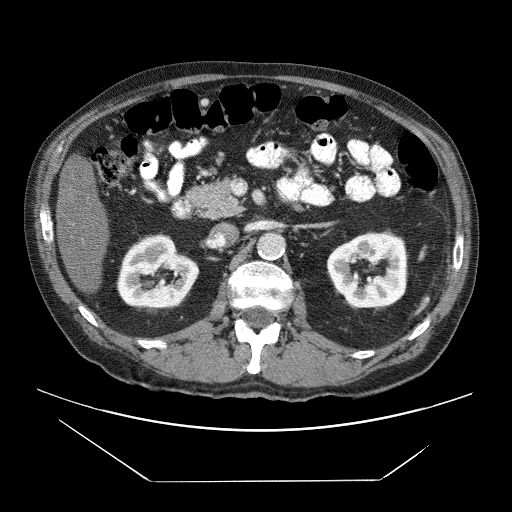
Contrast-enhanced abdominal CT (liver protocol), one axial slice; slice 17 of 83 in the series (ordered by position); 120 kVp; soft-tissue window (W 400 / L 40 HU); 2.5 mm slice thickness; 512 × 512 image matrix, field of view 420 × 420 mm. From the clinical record (not read from this slice): diagnosis: hepatocellular carcinoma (patient treated with transarterial chemoembolisation; whether this scan precedes or follows treatment is not stated here); TNM stage (as recorded): Stage-IVB; Child-Pugh class: B; tumour differentiation: poorly differentiated; tumour nodularity: uninodular.
Structures marked on this image (semi-automatically segmented with operator editing):
- liver parenchyma outside the tumour (the mass and vessels are separate outlines, so this box may not span the whole liver): bounding box [x1, y1, x2, y2] px = [56, 156, 110, 294]